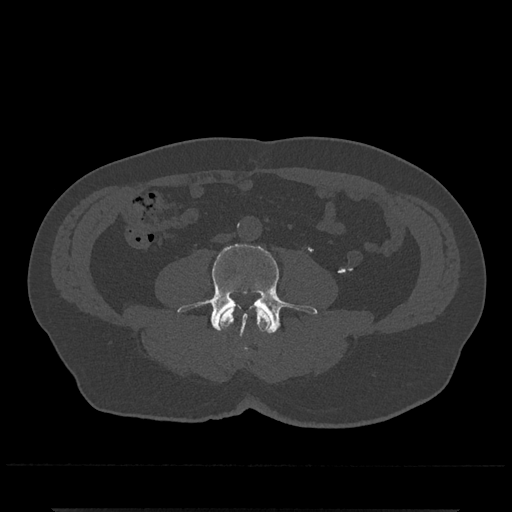
CT including the spine, one axial slice; position 171 of 797 along the scan axis; bone window (W 1800 / L 400 HU); 0.5 mm slice thickness; 512 × 512 image matrix. Male patient, age 67 years. From the clinical record (not read from this slice): primary cancer: prostate.
Outlined on this slice (semi-automatic segmentation, software-assisted and operator-edited):
- L3 vertebra: box from (x=219, y=306) to (x=272, y=350) px
- L4 vertebra: (x=178, y=243)–(x=317, y=334)